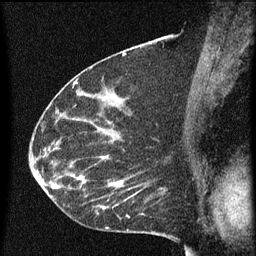
Breast MRI (dynamic contrast-enhanced), one sagittal slice; slice 35 of 60 in the series (ordered by position); dynamic contrast-enhanced series, image 2 of 3 at this slice position (ordered by acquisition); 1.5 T; TE 4.2 ms, TR 8 ms; 256 × 256 image matrix, field of view 180 × 180 mm. Patient: female, 55 years.
Annotated regions visible in this slice (semi-automatic segmentation, software-assisted and operator-edited):
- analysis volume of interest (the breast-tissue region the enhancement analysis was run in; not a lesion): box from (x=51, y=156) to (x=145, y=217) px
- tumour enhancement mask (voxels above the 70 % enhancement threshold inside the analysis volume of interest): (x=52, y=156)–(x=143, y=215)